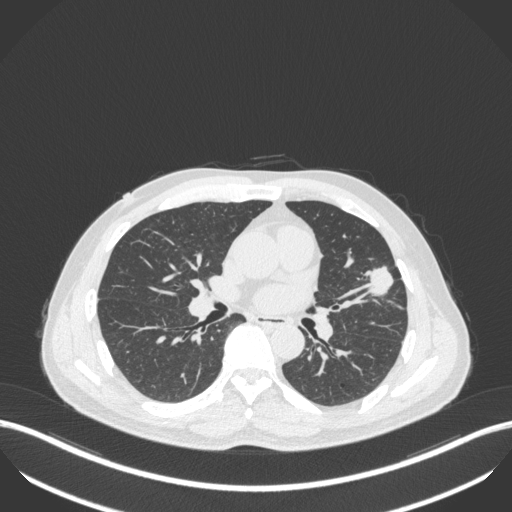
Chest CT, one axial slice. Slice 212 of 418 in the series (ordered by position). Reconstruction kernel B31f. 120 kVp. Lung window (W 1500 / L -600 HU). 1 mm slice thickness. 512 × 512 image matrix, field of view 400 × 400 mm. Male patient, age 55 years. From the clinical record (not read from this slice): clinical TNM (as recorded): T1c N0 M0; histopathological grade: G2-3.
Outlined on this slice (bounding box drawn by a radiologist):
- lung tumour (recorded histology: adenocarcinoma): bounding box <359,264,395,301> (left, top, right, bottom; pixels)